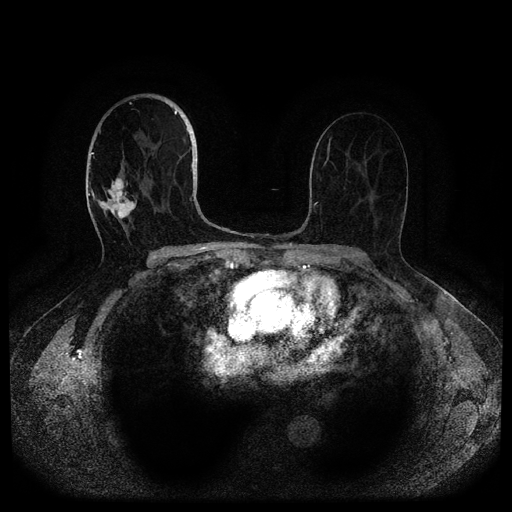
Breast MRI (dynamic contrast-enhanced, multi-phase), one axial slice; slice 58 of 116 in the series (ordered by position); dynamic contrast-enhanced series, time point 2 of 5 at this slice position (early post-contrast); 1.5 T; TE 2.6 ms, TR 5.3 ms; 2 mm slice thickness; 512 × 512 image matrix. Female patient, age 82 years.
Structures marked on this image (semi-automatically segmented with operator editing):
- breast lesion (labelled 'tumour' in the annotation; benign lesions carry a separate 'benign' label): box from (x=101, y=174) to (x=137, y=222) px